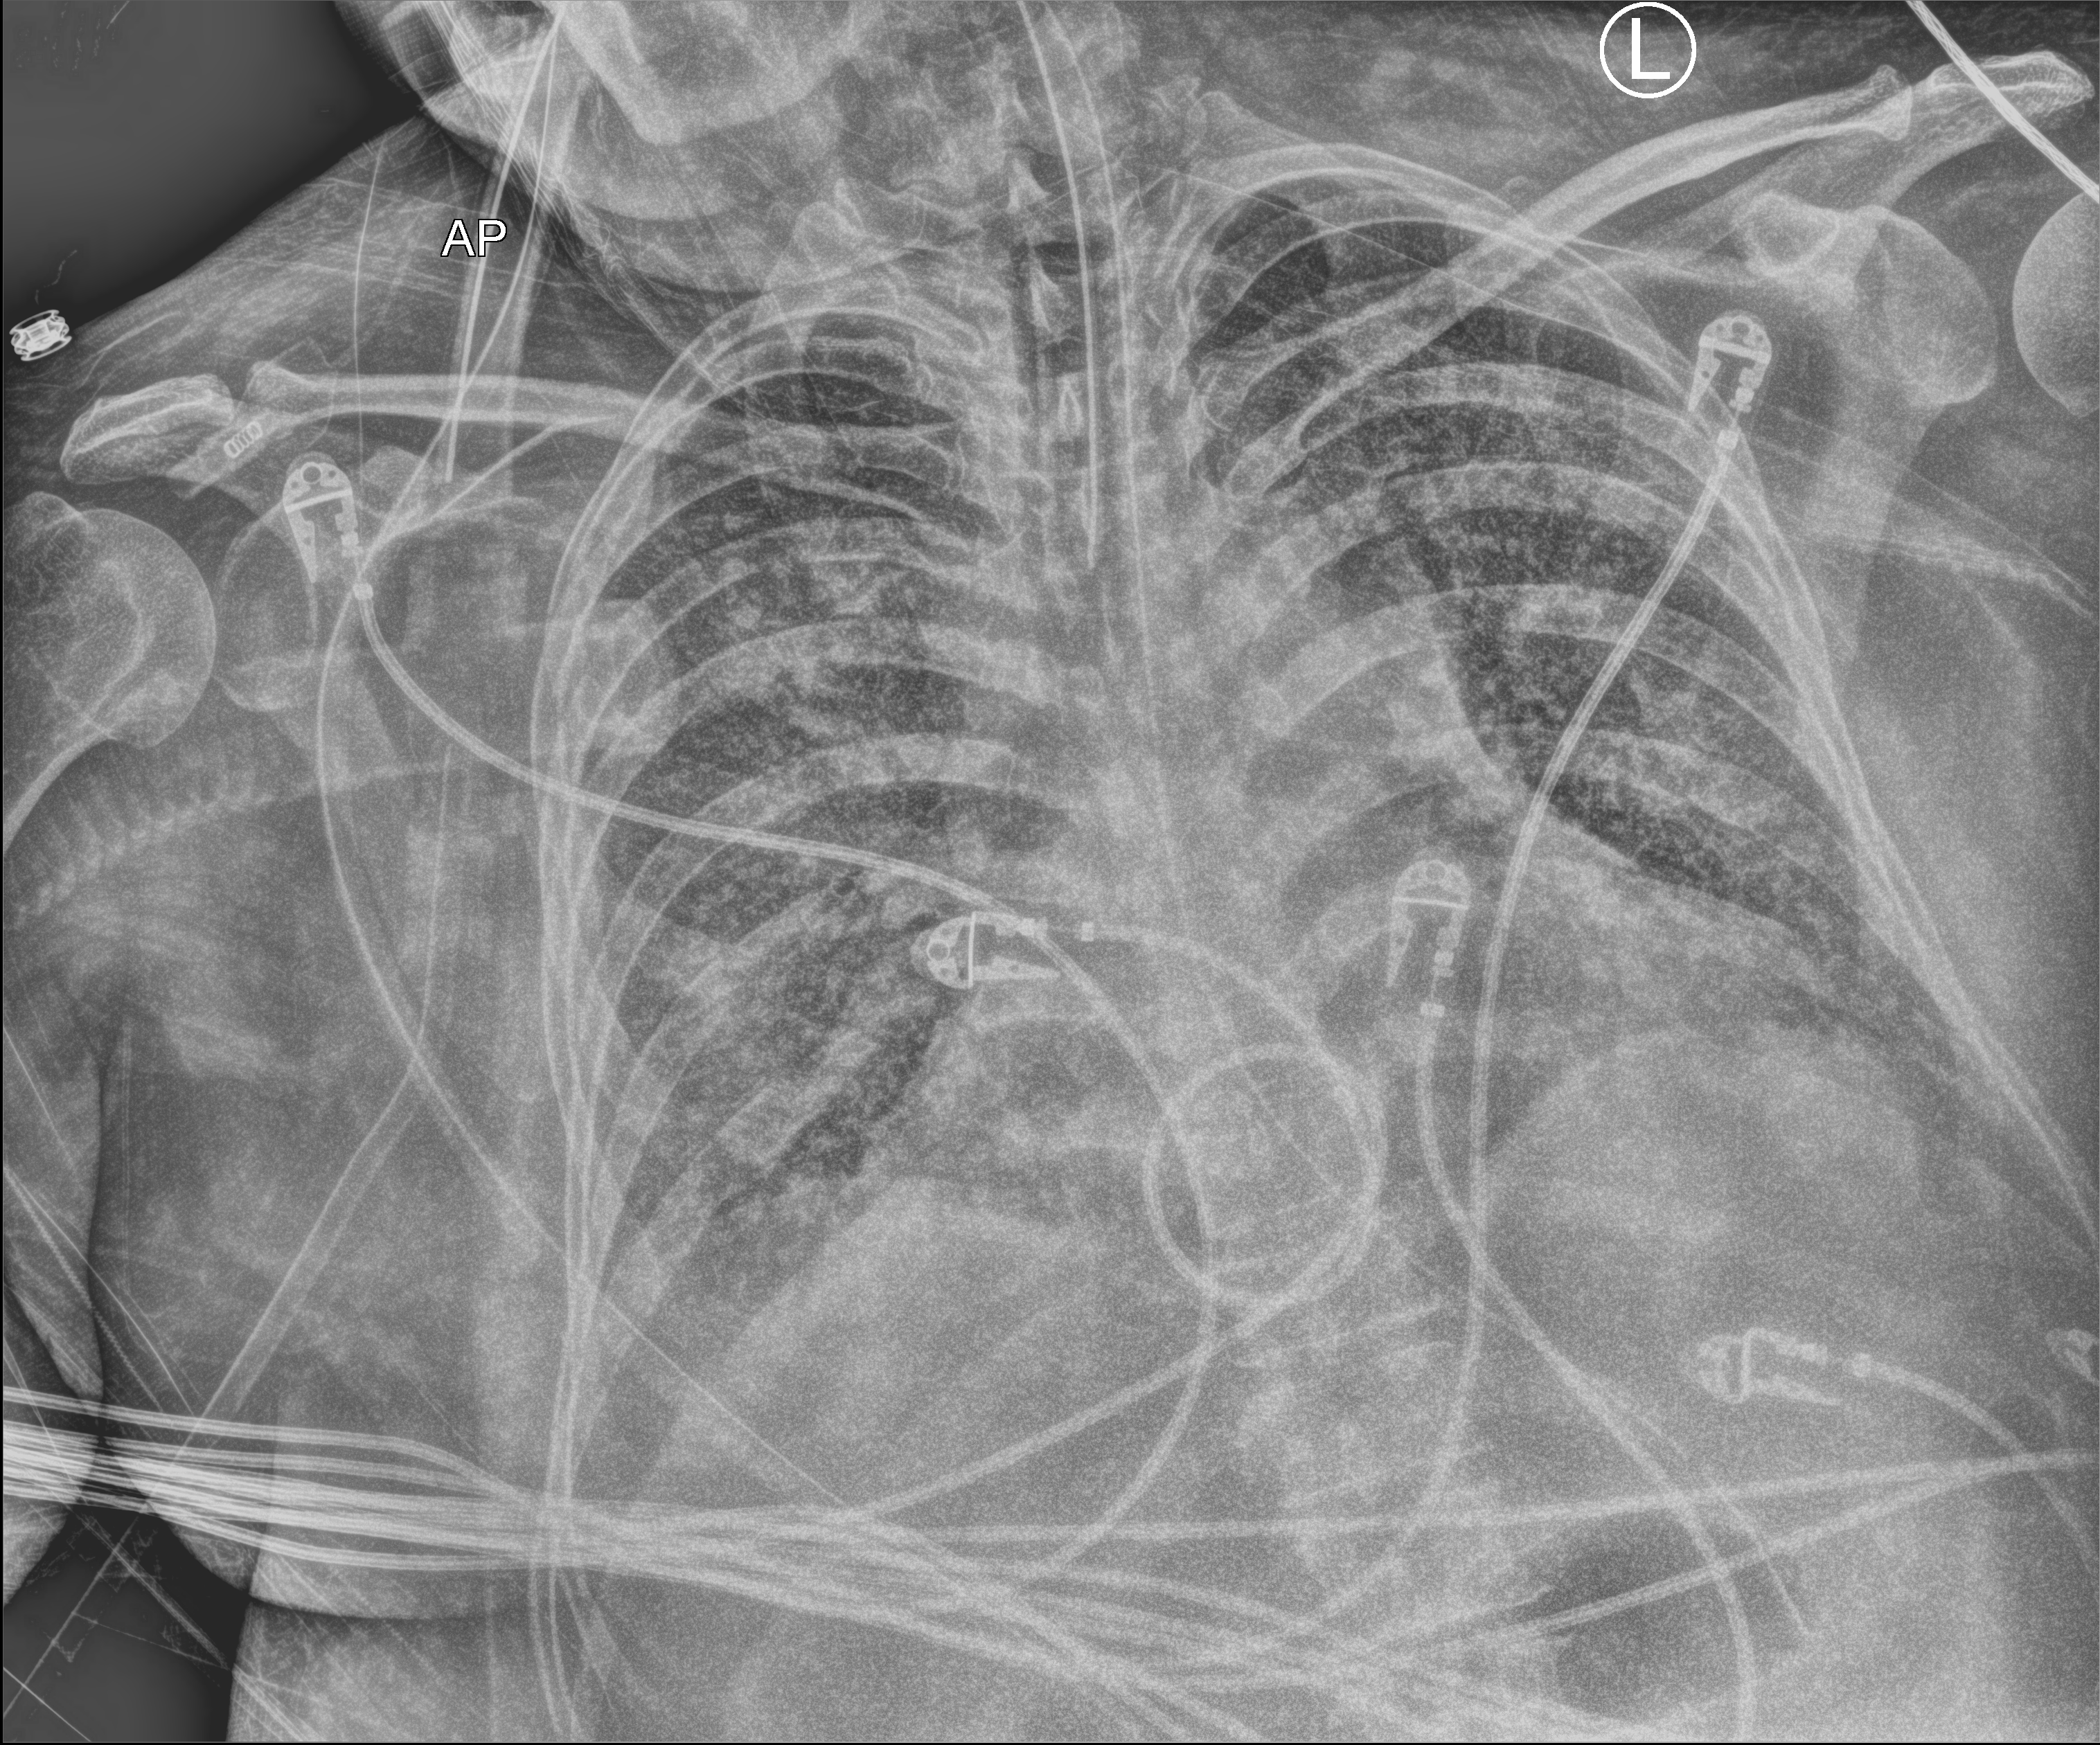
Portable chest radiograph. Patient hospitalised with COVID-19, aged 18–59 years.
Admission-level facts for this patient (not findings on this image; timing relative to this image not recorded): other chronic lung disease (admission record): no; chronic kidney disease (admission record): no; hypertension (admission record): no.